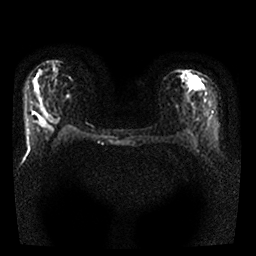
Breast MRI, one axial slice. Slice 12 of 25 in the series (ordered by position). Diffusion-weighted series; image 2 of 4 stored at this slice position (different b-values; order by instance number). 1.5 T. 4 mm slice thickness. 256 × 256 image matrix. Female patient.
Annotated regions visible in this slice (manually delineated by an expert):
- tumour on diffusion-weighted imaging: bounding box (x1, y1, x2, y2) in pixels: (188, 76, 203, 91)